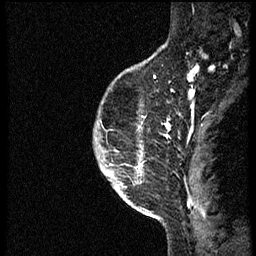
Breast MRI (dynamic contrast-enhanced), one sagittal slice; position 46 of 56 along the scan axis; dynamic contrast-enhanced study with each time point stored as its own series, time point 2 of 3 at this slice position (early post-contrast, ordered by acquisition time); 1.5 T; TE 4.2 ms, TR 21.3 ms; 256 × 256 image matrix. Female patient, age 41 years. From the clinical record (not read from this slice): setting: breast cancer imaged before/during neoadjuvant chemotherapy; receptor status: HER2-positive.
Structures marked on this image (semi-automatically segmented with operator editing):
- analysis volume of interest (the breast-tissue region the enhancement analysis was run in; not a lesion): bounding box <120,73,175,205> (left, top, right, bottom; pixels)
- tumour enhancement mask (voxels above the 100 % enhancement threshold inside the analysis volume of interest): <141,122,171,153>